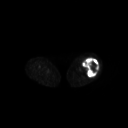
FDG PET of an extremity soft-tissue mass (from a PET/CT study), one axial slice. Position 215 of 267 along the scan axis. 3.27 mm slice thickness. 128 × 128 image matrix, field of view 700 × 700 mm. Patient: female, 62 years. Case-level facts recorded for this patient, not image findings: histological type: undifferentiated – high grade; grade: high; site of the primary tumour: left thigh.
Annotated regions visible in this slice (expert contour drawn on MRI and transferred to this co-registered scan by the dataset authors):
- gross tumour volume including surrounding oedema: bounding box <82,58,99,77> (left, top, right, bottom; pixels)
- gross tumour volume (mass): <82,58,99,77>